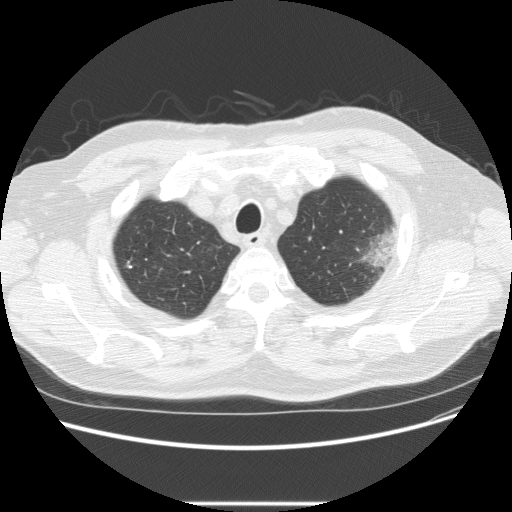
Low-dose screening chest CT, one axial slice. Reconstruction kernel STANDARD. 120 kVp. Lung window (W 1500 / L -600 HU). 2.5 mm slice thickness. 512 × 512 image matrix, field of view 380 × 380 mm.
Outlined on this slice (outlined manually by an expert reader):
- lesion 1 (tumor, upper lobe of left lung): bounding box <364,231,398,270> (left, top, right, bottom; pixels)